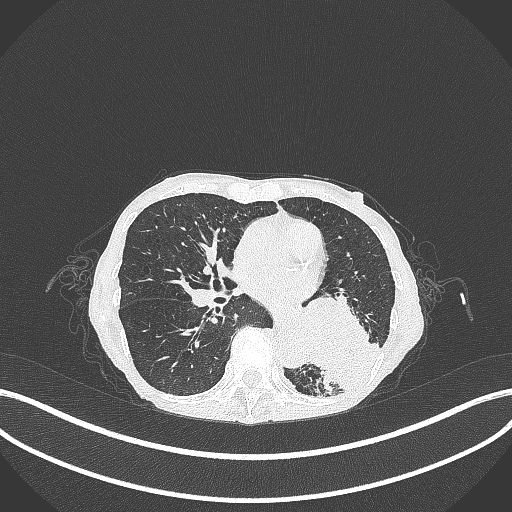
Chest CT, one axial slice; position 128 of 347 along the scan axis; 120 kVp; lung window (W 1500 / L -600 HU); 512 × 512 image matrix, field of view 400 × 400 mm. Female patient, age 70 years. From the clinical record (not read from this slice): clinical TNM (as recorded): T3 N0 M0.
Annotated regions visible in this slice (bounding box drawn by a radiologist):
- lung tumour (recorded histology: small cell carcinoma): box from (x=293, y=286) to (x=385, y=397) px